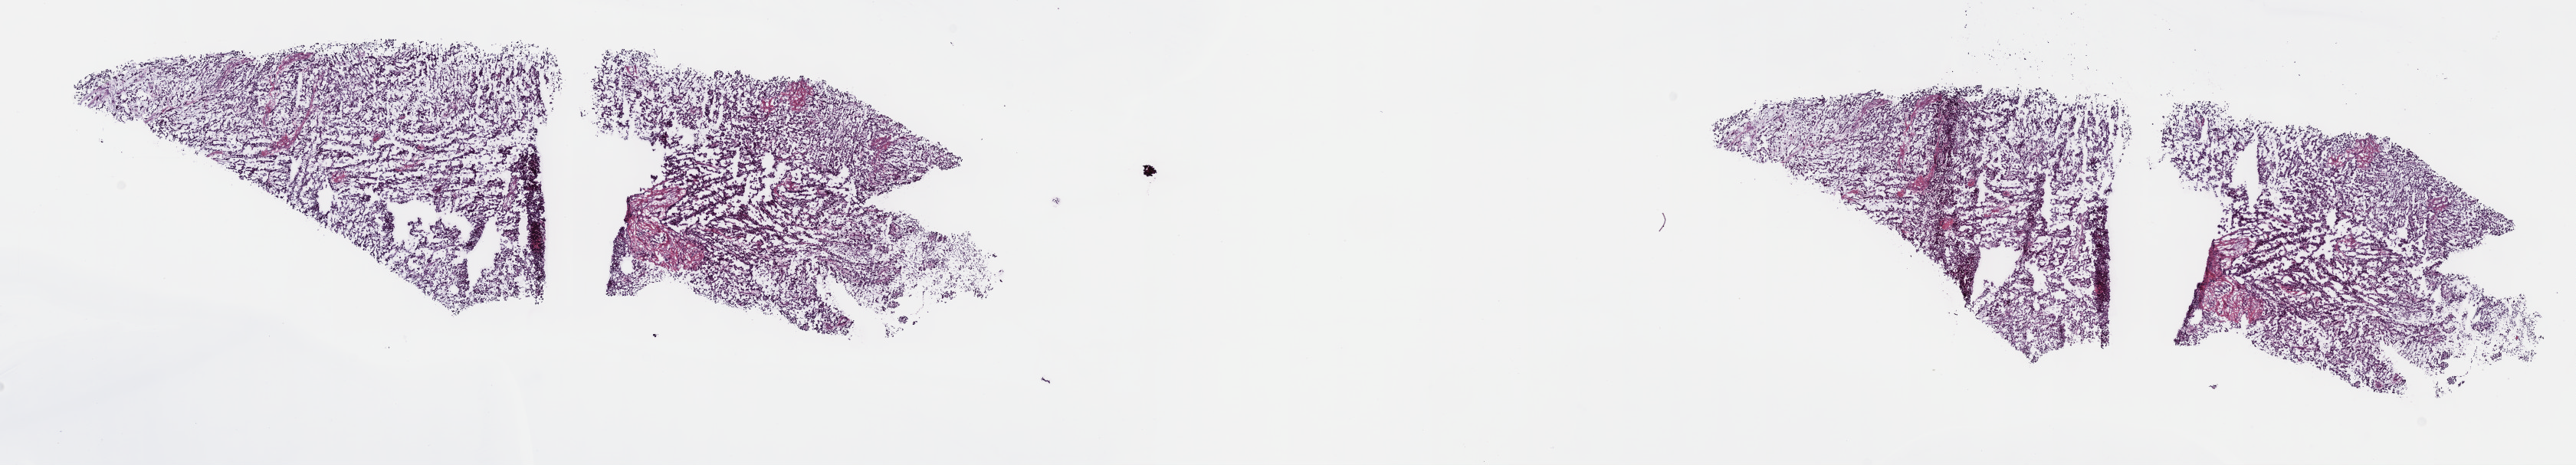
Whole-slide histology image, Hematoxylin and eosin (H&E) stained, low-resolution overview of the scanned area, about 27.2 x 4.9 mm (from a 40x scan). Frozen section from the top of the tissue portion. Sample: primary tumour, mesothelium. Male patient; age at initial diagnosis 67 years. Composition of this section per pathologist review: tumour cells 90%, tumour nuclei 90%, normal cells 0%, stromal cells 10%, necrosis 0%. Inflammatory infiltration, as recorded: lymphocyte infiltration 40%, monocyte infiltration 20%, neutrophil infiltration 20%.
Histologic diagnosis: Epithelioid mesothelioma, malignant (pleura, NOS). AJCC pathologic stage: III (7th edition).